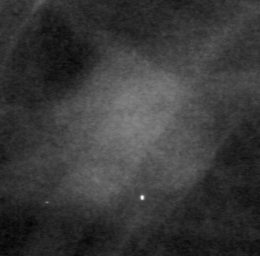
Crop from a digitized film mammogram around one marked abnormality, left breast, CC view.
- Mass, shape round, margins obscured; BI-RADS assessment category 0 (incomplete: needs additional imaging); pathology result (as recorded, not read from the image): benign.